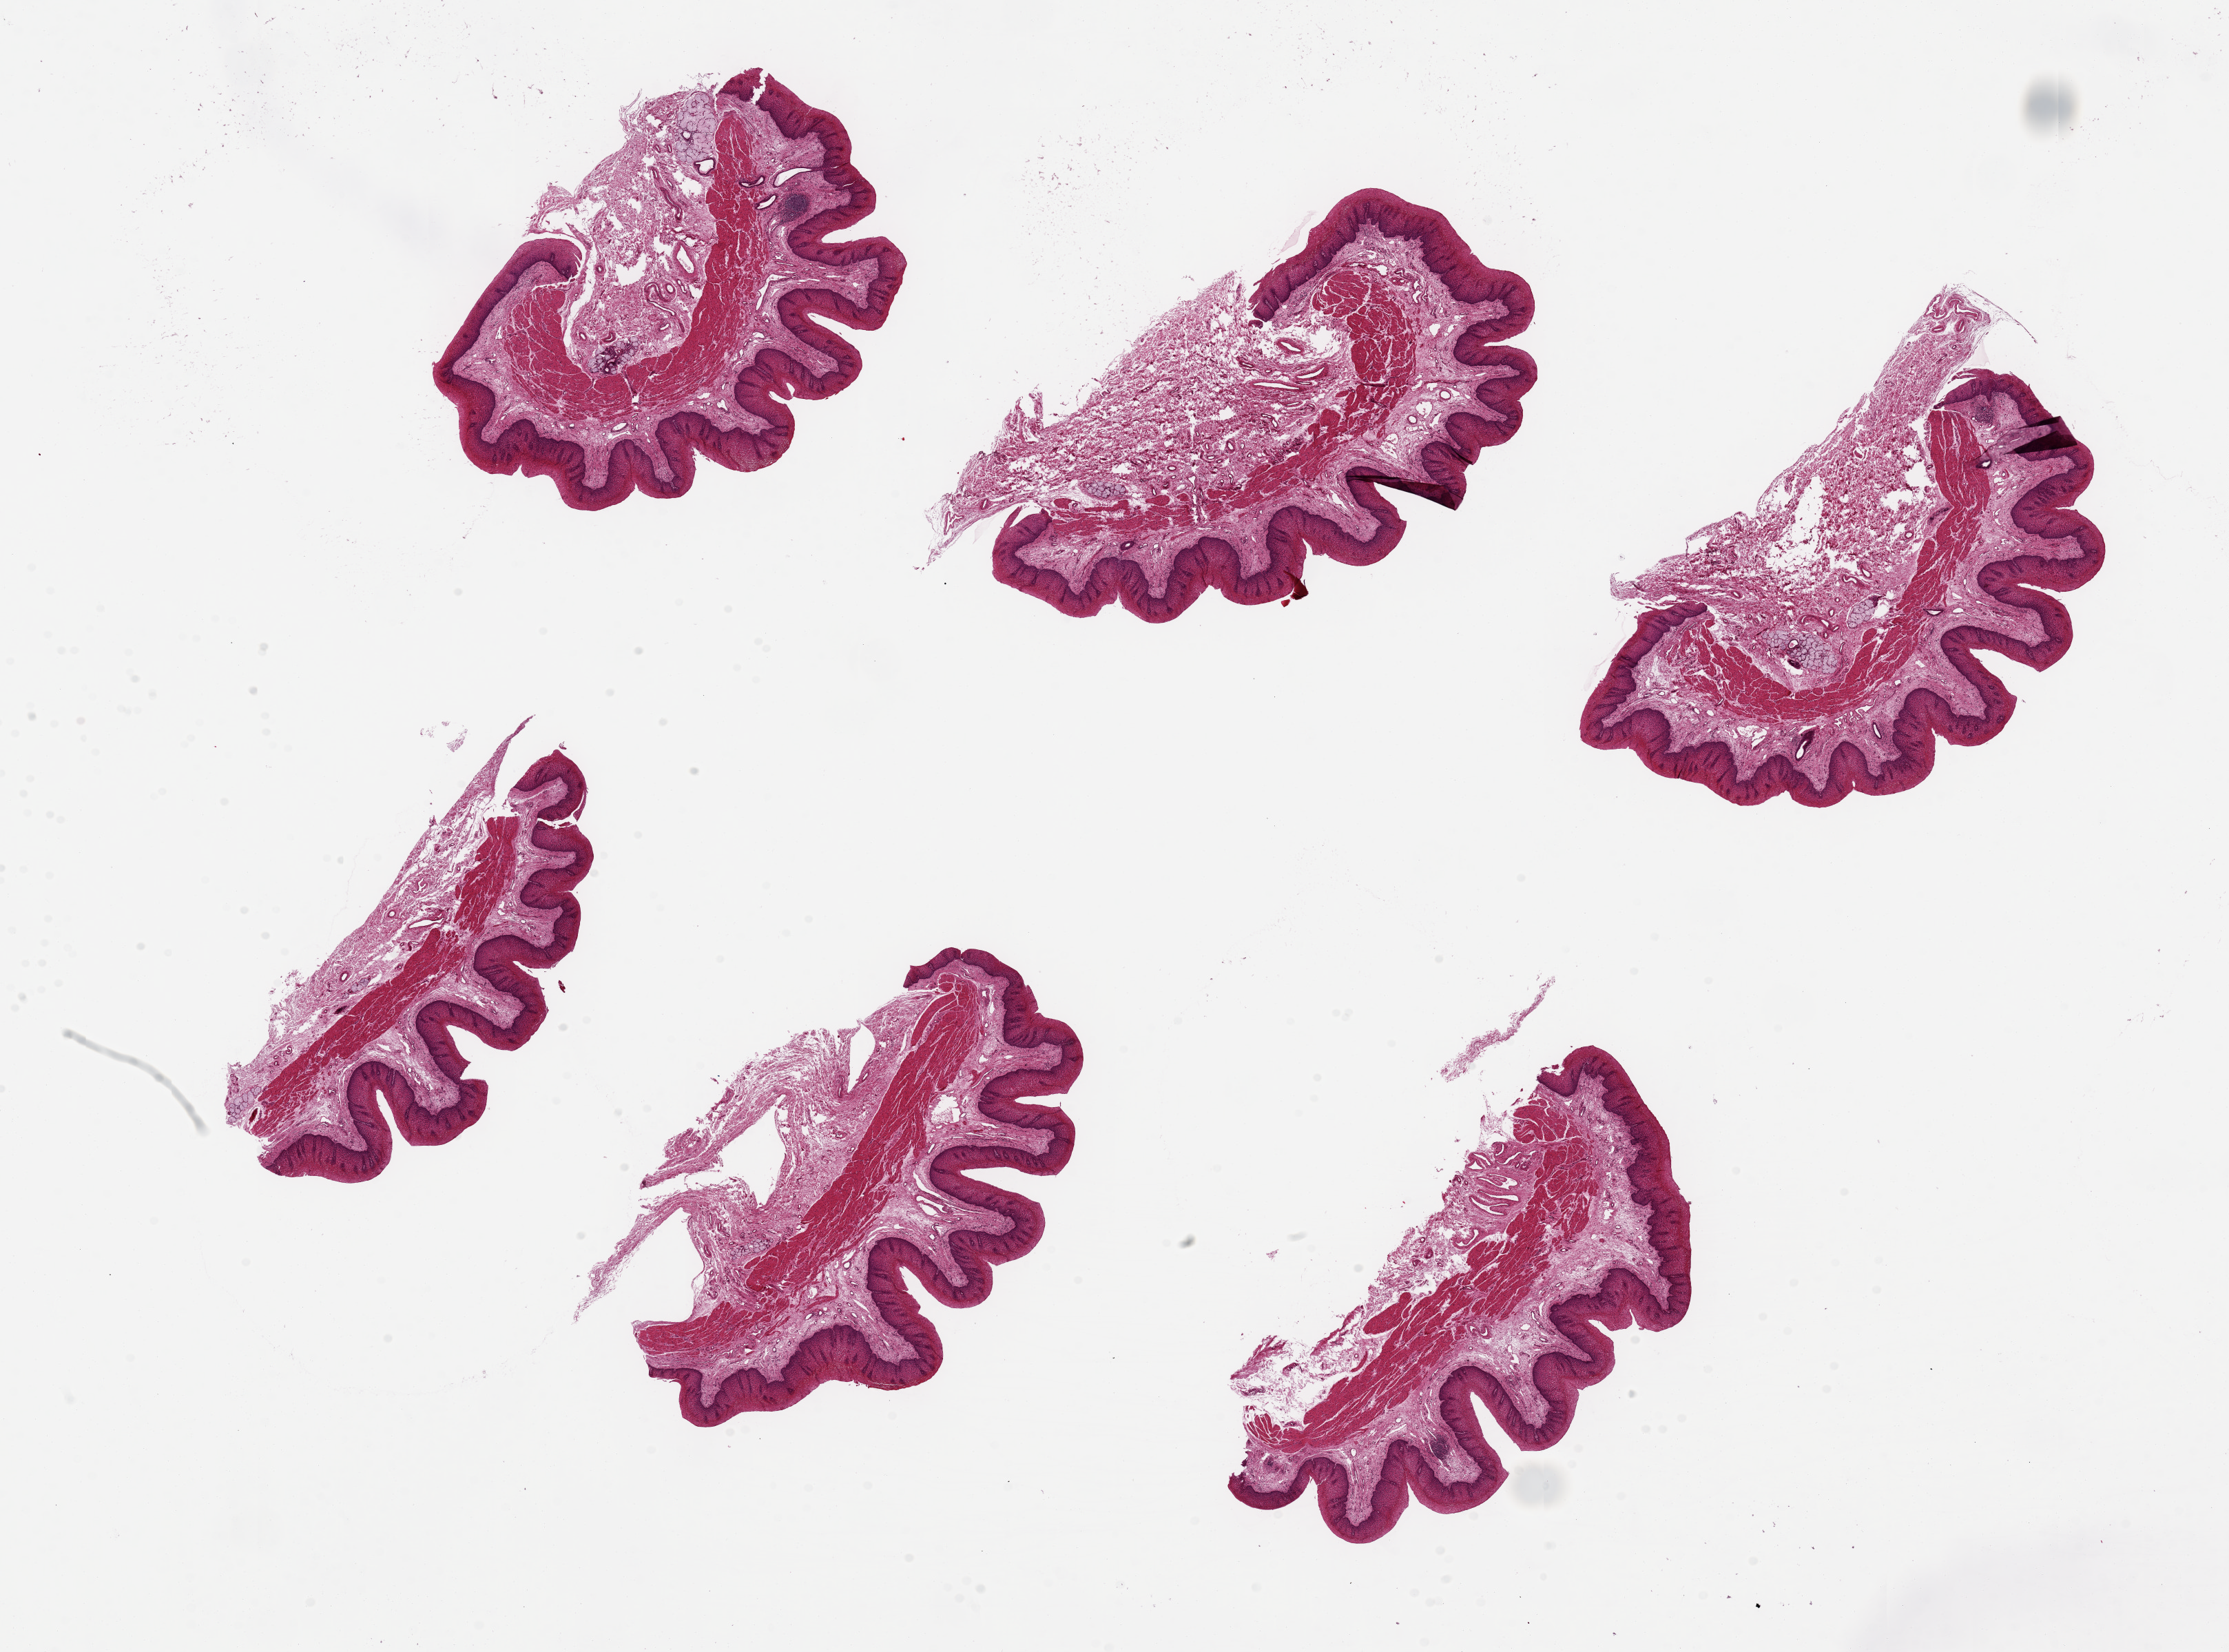
Digitized H&E-stained section, brightfield — shown as a low-resolution overview of the whole scanned area (about 25.6 x 19.0 mm, from a 20x scan), PAXgene-fixed paraffin-embedded (PFPE) section, sampled site (target tissue): esophageal mucous membrane, donor tissue sample. Male donor.
* review note (as recorded): 6 pieces, up to 6.6x4 mm; well preserved mucosa